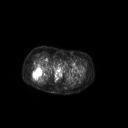
FDG PET of an extremity soft-tissue mass (from a PET/CT study), one axial slice; position 58 of 267 along the scan axis; 3.27 mm slice thickness; 128 × 128 image matrix, field of view 700 × 700 mm. Female patient, age 70 years. From the clinical record (not read from this slice): histological type: synovial sarcoma; grade: intermediate; site of the primary tumour: right buttock.
Outlined on this slice (expert contour drawn on MRI and transferred to this co-registered scan by the dataset authors):
- gross tumour volume including surrounding oedema: box from (x=32, y=66) to (x=44, y=81) px
- gross tumour volume (mass): (x=32, y=66)–(x=43, y=79)